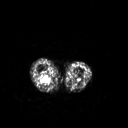
FDG PET of an extremity soft-tissue mass (from a PET/CT study), one axial slice. Slice 186 of 267 in the series (ordered by position). 3.27 mm slice thickness. 128 × 128 image matrix, field of view 500 × 500 mm. Patient: female, 62 years. From the clinical record (not read from this slice): histological type: liposarcoma; site of the primary tumour: right thigh.
Annotated regions visible in this slice (expert contour drawn on MRI and transferred to this co-registered scan by the dataset authors):
- gross tumour volume (mass): box from (x=38, y=74) to (x=52, y=85) px